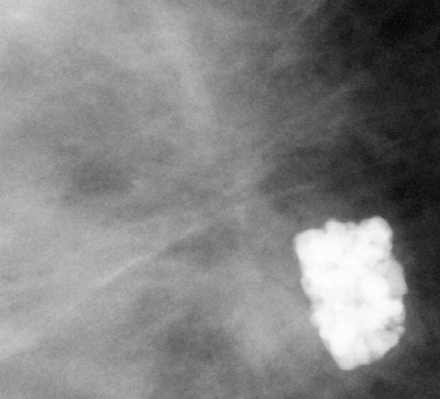
Crop from a digitized film mammogram around one marked abnormality, right breast, CC view, BI-RADS breast density category 3 (scale 1–4).
Marked abnormality: mass, shape irregular, margins spiculated; BI-RADS assessment category 5; subtlety rating 4 on a 1 (subtle) to 5 (obvious) scale; pathology result (as recorded, not read from the image): malignant.